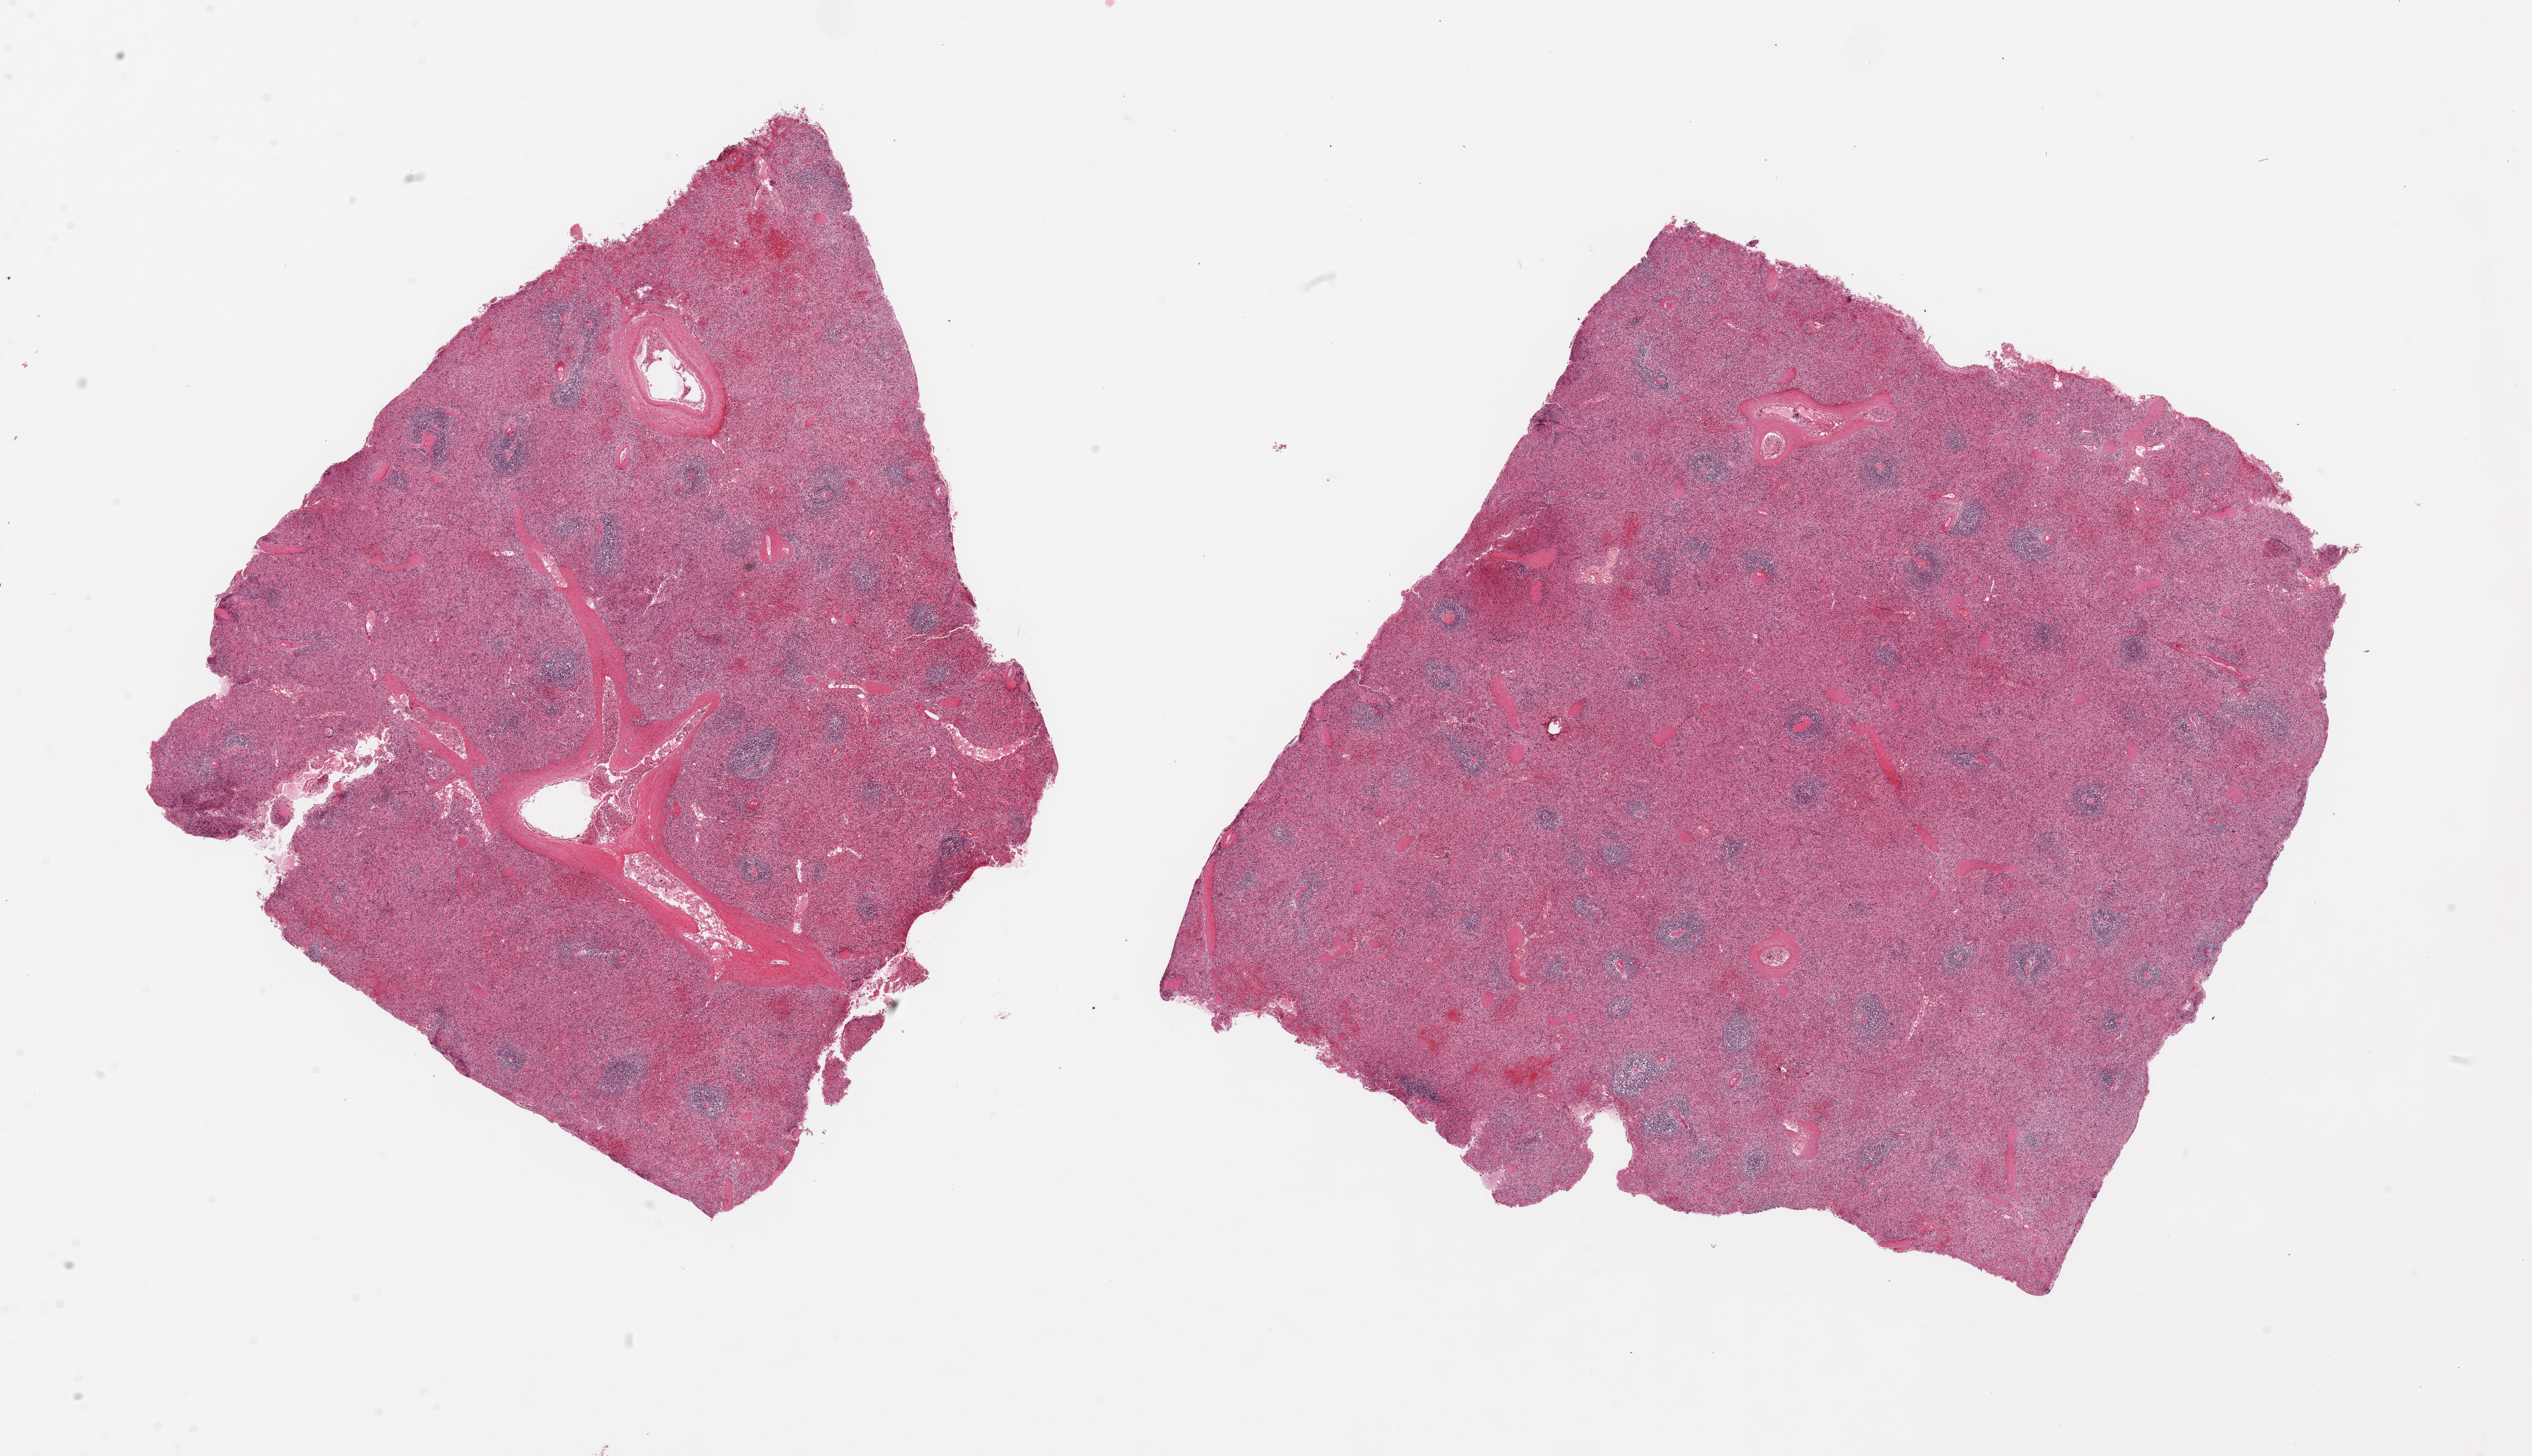
Digitized H&E-stained section, brightfield — whole scanned area (about 28.5 x 16.4 mm) shown as a low-resolution overview; PAXgene-fixed paraffin-embedded (PFPE) section; section of spleen (target tissue); tissue donor sample. Donor: male.
- reviewer comment on this tissue sample: 2 pieces; mild congestion